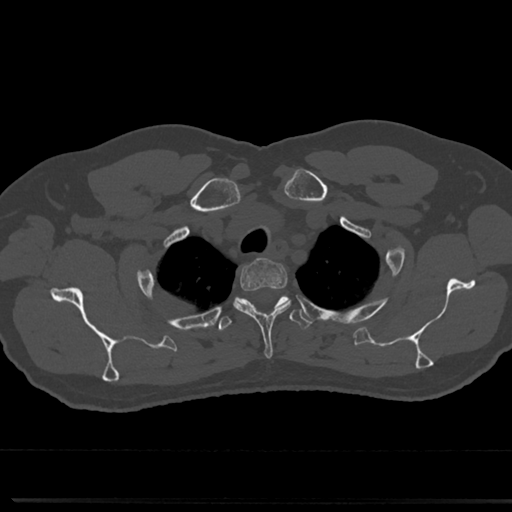
CT including the spine, one axial slice. Reconstruction kernel Br40s/3. 120 kVp. Bone window (W 1800 / L 400 HU). 512 × 512 image matrix. Patient: male, 61 years. Case-level facts recorded for this patient, not image findings: primary cancer: prostate.
Structures marked on this image (semi-automatic segmentation, software-assisted and operator-edited):
- T2 vertebra: bounding box (x1, y1, x2, y2) in pixels: (235, 260, 288, 342)
- T3 vertebra: (215, 293, 313, 333)